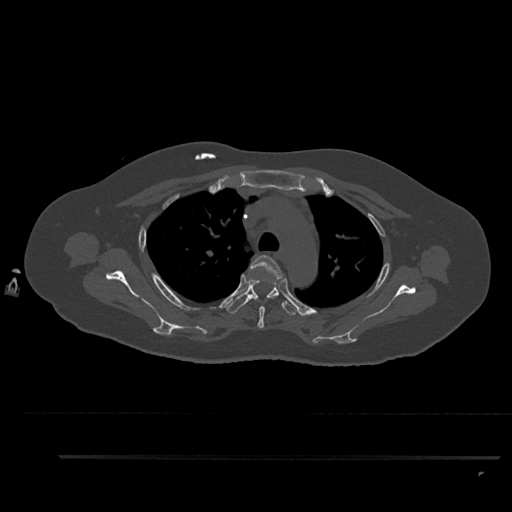
CT including the spine, one axial slice. Slice 661 of 797 in the series (ordered by position). 120 kVp. Bone window (W 1800 / L 400 HU). 0.5 mm slice thickness. 512 × 512 image matrix, field of view 408 × 408 mm. Female patient, age 44 years. Case-level facts recorded for this patient, not image findings: primary cancer: renal.
Annotated regions visible in this slice (semi-automatic segmentation, software-assisted and operator-edited):
- T3 vertebra: box from (x=250, y=255) to (x=283, y=329) px
- T4 vertebra: (x=226, y=279)–(x=298, y=315)